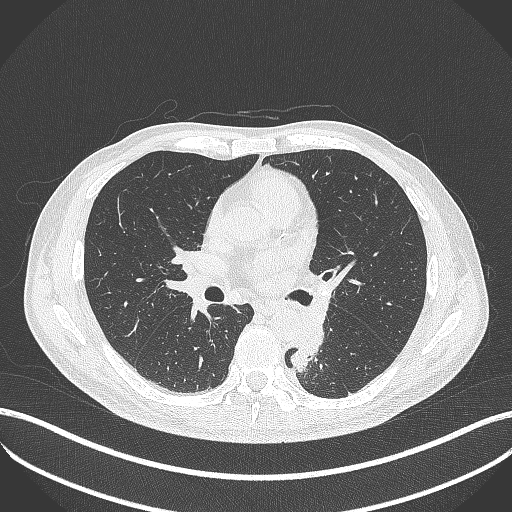
Chest CT, one axial slice. Slice 221 of 451 in the series (ordered by position). 120 kVp. Lung window (W 1500 / L -600 HU). 1 mm slice thickness. 512 × 512 image matrix, field of view 400 × 400 mm. Patient: male, 72 years. From the clinical record (not read from this slice): clinical TNM (as recorded): T2b N0 M1.
Outlined on this slice (bounding box drawn by a radiologist):
- lung tumour (recorded histology: adenocarcinoma): box from (x=289, y=329) to (x=330, y=376) px